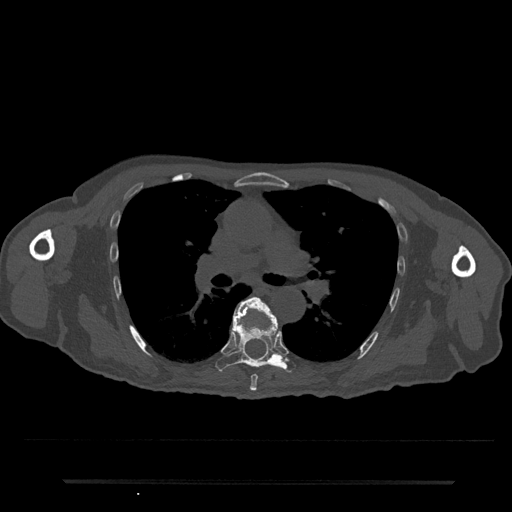
CT including the spine, one axial slice; slice 497 of 797 in the series (ordered by position); reconstruction kernel Br40s/3; bone window (W 1800 / L 400 HU); 0.5 mm slice thickness; 512 × 512 image matrix, field of view 427 × 427 mm. Male patient, age 74 years. Case-level facts recorded for this patient, not image findings: primary cancer: prostate.
Structures marked on this image (semi-automatic segmentation, software-assisted and operator-edited):
- T6 vertebra: bounding box [x1, y1, x2, y2] px = [233, 296, 278, 391]
- T7 vertebra: [216, 305, 295, 372]